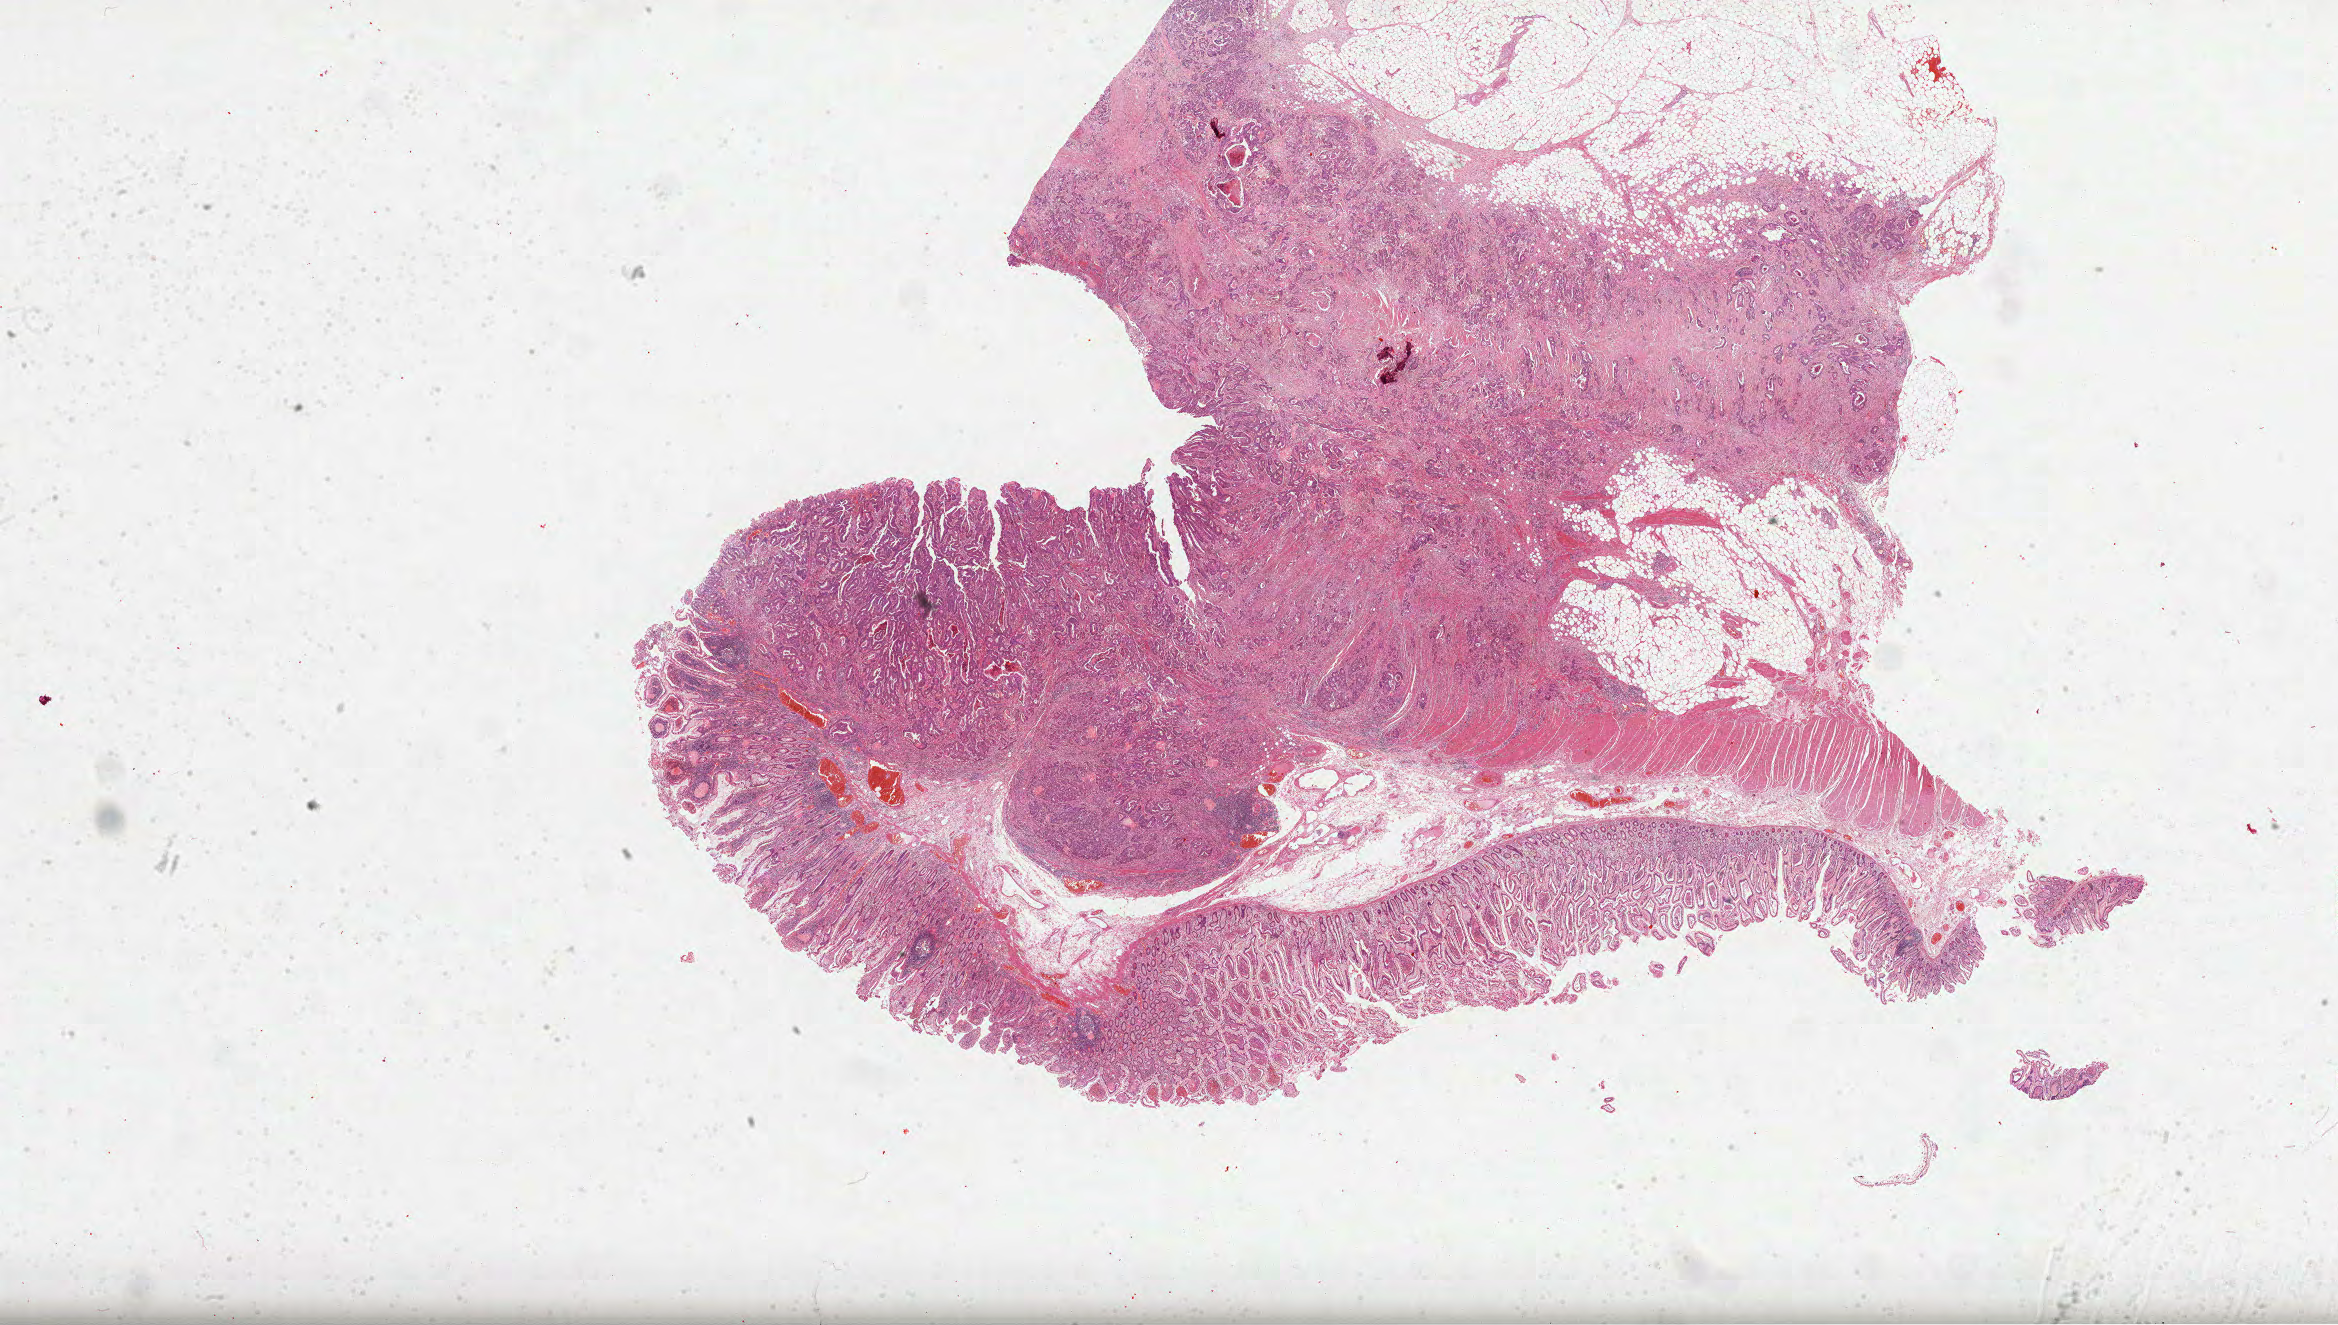
Whole-slide histology image, Hematoxylin and eosin (H&E) stained — whole scanned area (about 37.7 x 21.4 mm, slide scanned at 40x) shown as a low-resolution overview. Formalin-fixed paraffin-embedded (FFPE) diagnostic section. Sample: primary tumour, colon. Female patient; age at initial diagnosis 60 years.
AJCC pathologic stage: IIIB. Histologic diagnosis: Adenocarcinoma, NOS.